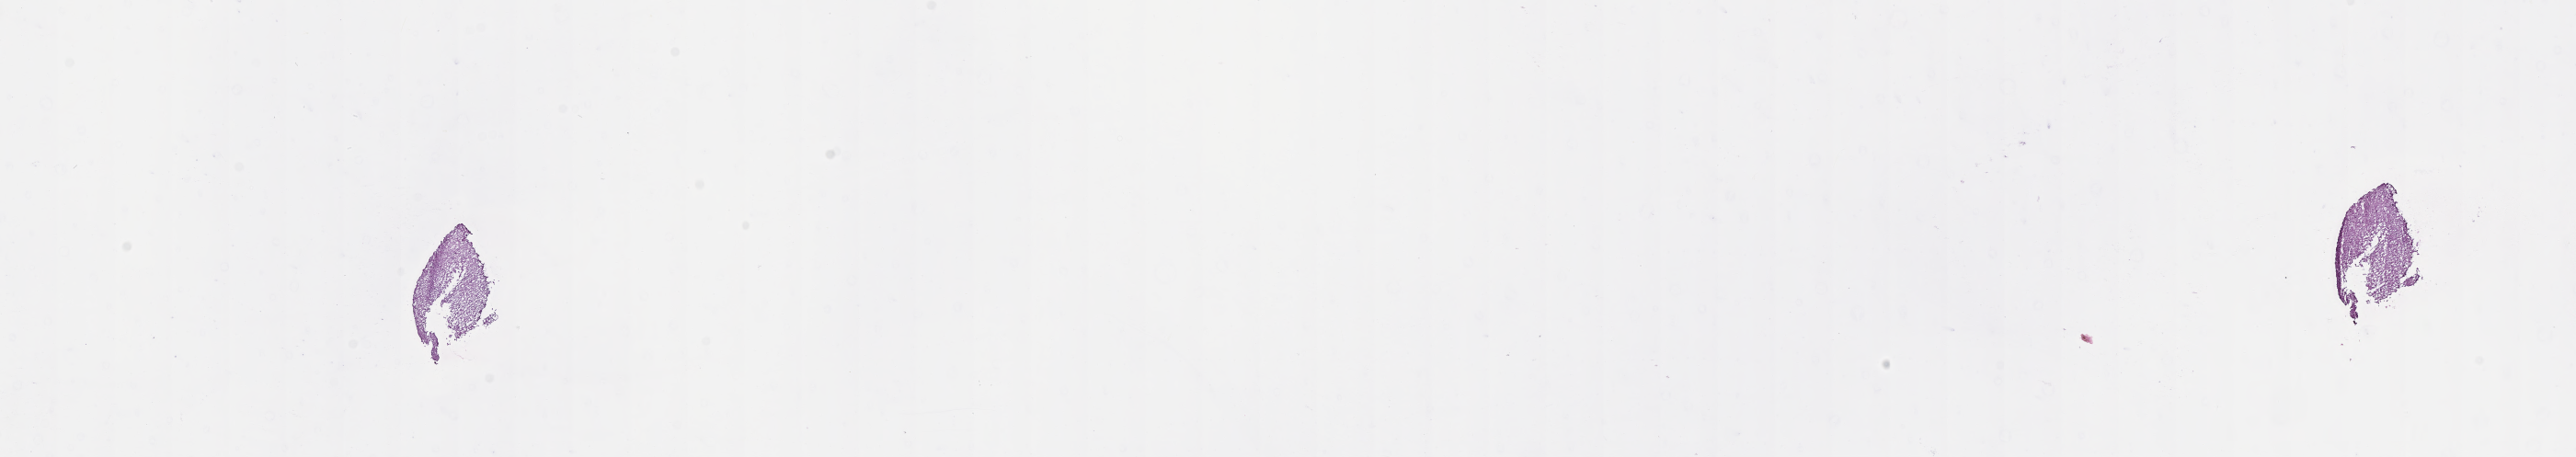
Digitized haematoxylin and eosin-stained section of tumor tissue from the frontal lobe — shown as a low-resolution overview of the whole scanned area (about 22.6 x 4.0 mm). Frozen section. Patient: female, age 168 months (14 years).
Recorded diagnosis: Ganglioglioma, NOS.